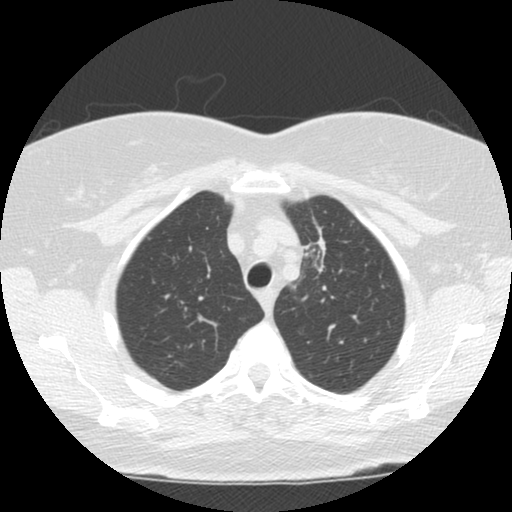
Low-dose screening chest CT, one axial slice. Position 95 of 120 along the scan axis. Reconstruction kernel STANDARD. 120 kVp. Lung window (W 1500 / L -600 HU). 2.5 mm slice thickness. 512 × 512 image matrix.
Structures marked on this image (expert manual segmentation):
- lesion 1 (tumor, upper lobe of left lung): bounding box (x1, y1, x2, y2) in pixels: (303, 225, 326, 259)